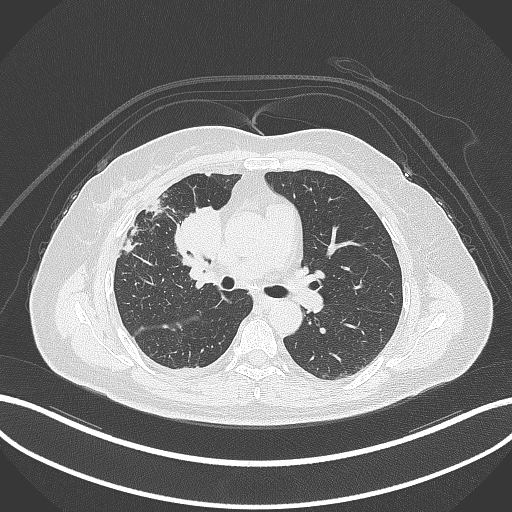
Chest CT, one axial slice. Position 164 of 305 along the scan axis. Reconstruction kernel B70f. 120 kVp. Lung window (W 1500 / L -600 HU). 512 × 512 image matrix. Female patient, age 52 years. From the clinical record (not read from this slice): clinical TNM (as recorded): T3 N1 M1.
Annotated regions visible in this slice (rectangle marked by the reading radiologist):
- lung tumour (recorded histology: adenocarcinoma): box from (x=168, y=198) to (x=228, y=271) px